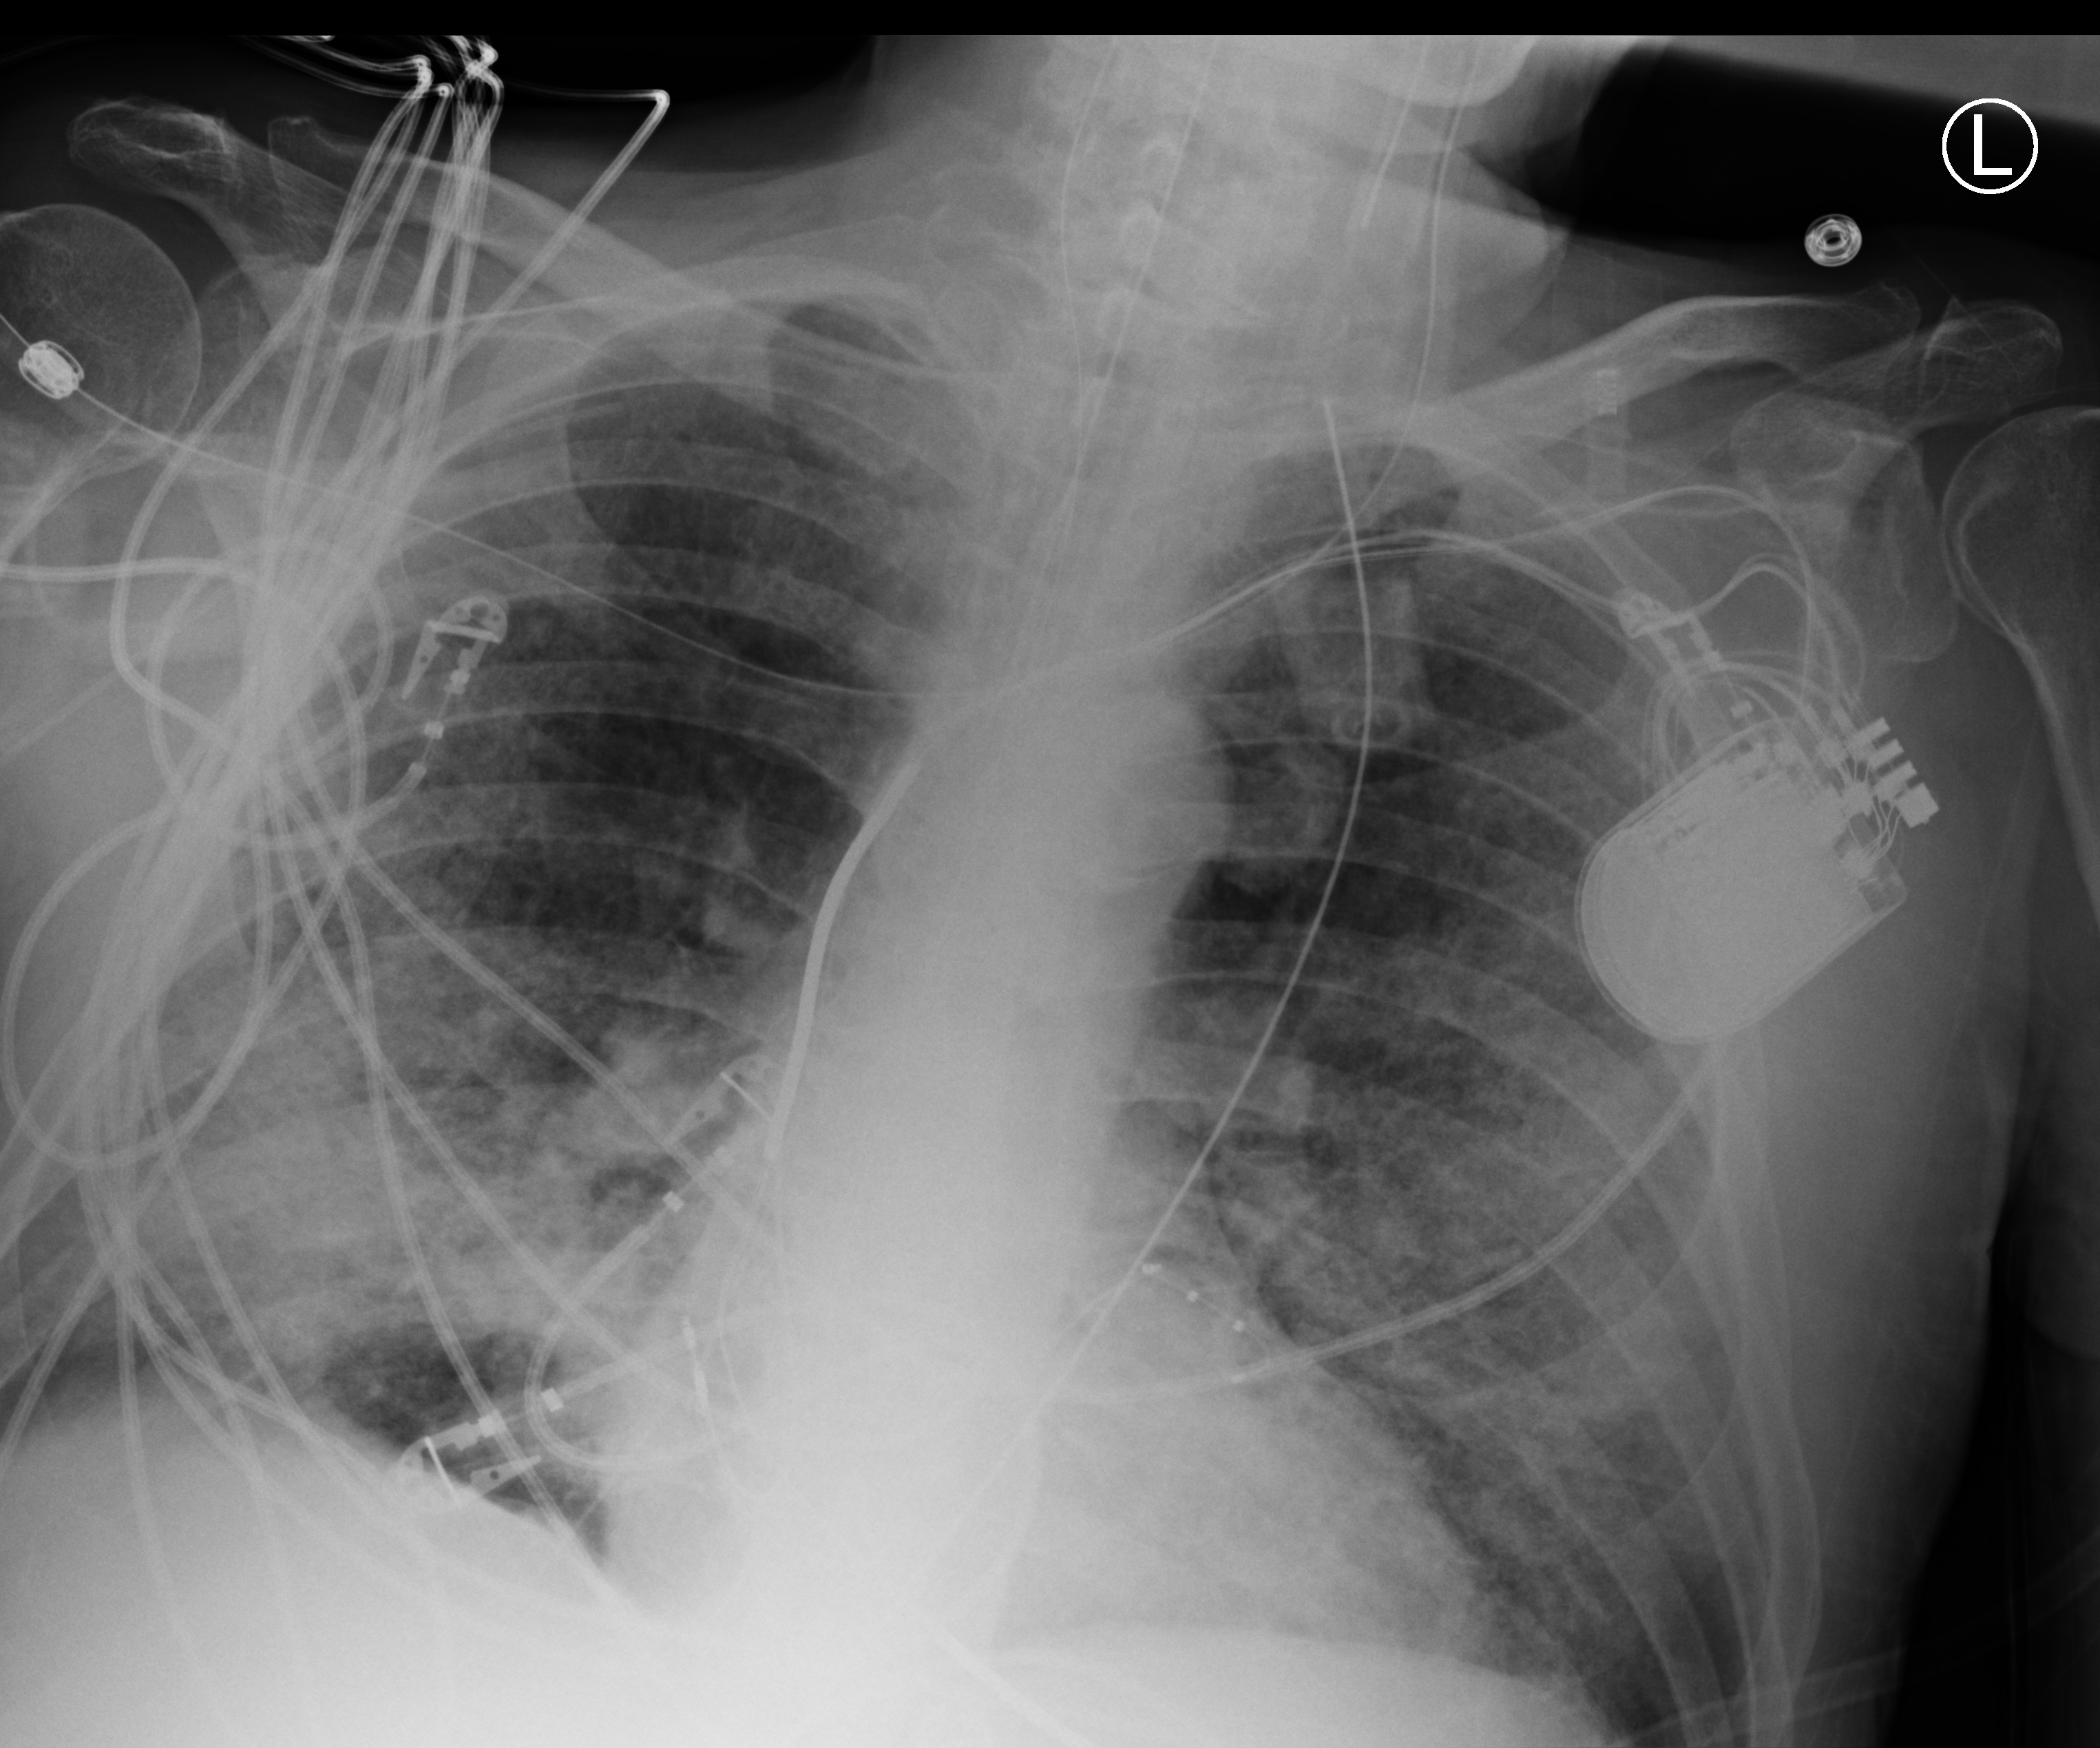
Chest X-ray (portable). Patient hospitalised with COVID-19; male, aged 60–74 years.
Hospital-stay facts (about this admission, not read from this image; timing relative to this image not recorded):
- COPD (admission record): no